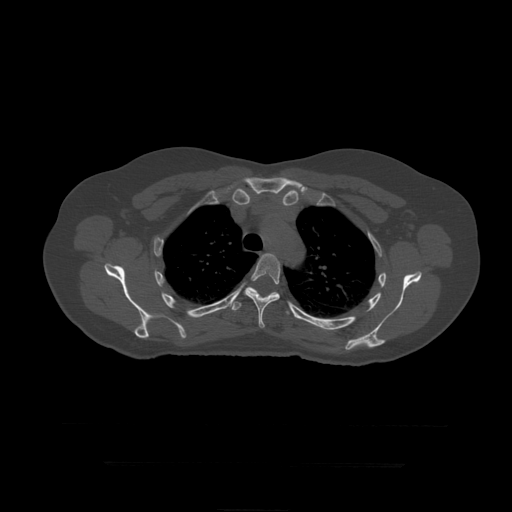
CT including the spine, one axial slice. Slice 333 of 399 in the series (ordered by position). Reconstruction kernel STANDARD. 120 kVp. Bone window (W 1800 / L 400 HU). 1.25 mm slice thickness. 512 × 512 image matrix, field of view 450 × 450 mm. Patient age 41 years. Case-level facts recorded for this patient, not image findings: primary cancer: breast.
Structures marked on this image (semi-automatically segmented with operator editing):
- T5 vertebra: bounding box <244,254,281,329> (left, top, right, bottom; pixels)
- T6 vertebra: <232,287,290,315>